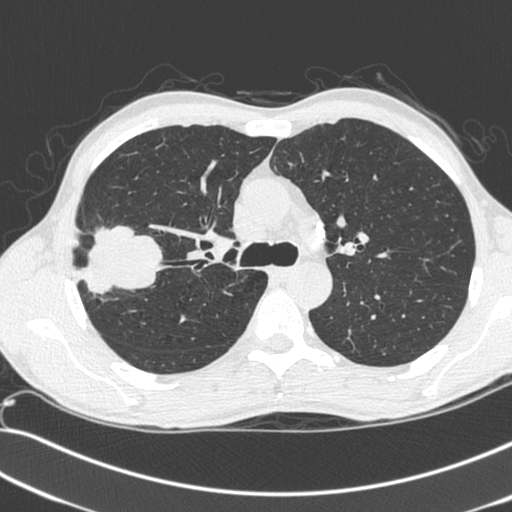
Axial slice from a low-dose chest CT screening exam, baseline annual screen, lung window (W 1500 / L -600 HU), 1.3 mm slice thickness, standard (soft-tissue) reconstruction kernel (C), 512 × 512 image matrix. Male participant, aged 55 years at enrolment. Current smoker at enrolment.
• Expert-annotated lung lesion, box from (x=69, y=228) to (x=153, y=303) px.
• Screening reader's record for this exam (one nodule recorded; not confirmed to be the boxed lesion): non-calcified nodule or mass ≥4 mm, right upper lobe, 52 × 39 mm, spiculated (stellate) margins, soft tissue attenuation.